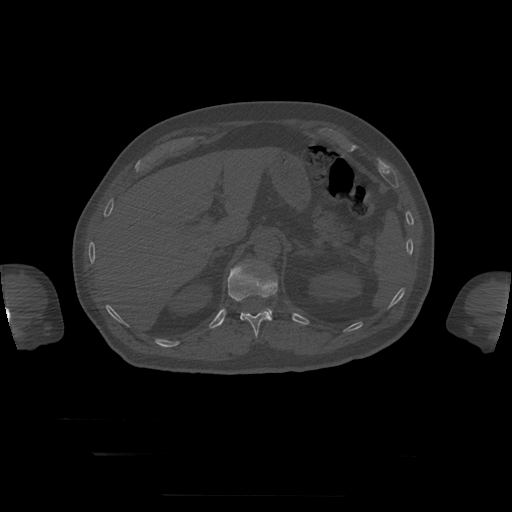
CT including the spine, one axial slice. Slice 69 of 397 in the series (ordered by position). 120 kVp. Bone window (W 1800 / L 400 HU). 512 × 512 image matrix, field of view 510 × 510 mm. Patient age 73 years. Case-level facts recorded for this patient, not image findings: primary cancer: prostate.
Outlined on this slice (semi-automatically segmented with operator editing):
- L1 vertebra: box from (x=267, y=309) to (x=272, y=315) px
- T12 vertebra: (x=228, y=264)–(x=278, y=338)